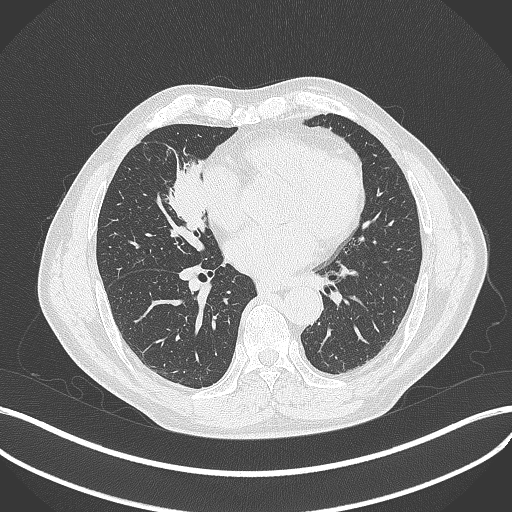
Chest CT, one axial slice; position 176 of 429 along the scan axis; reconstruction kernel B70f; 120 kVp; lung window (W 1500 / L -600 HU); 1 mm slice thickness; 512 × 512 image matrix. Patient: male, 61 years. Case-level facts recorded for this patient, not image findings: clinical TNM (as recorded): T2b N1 M0.
Annotated regions visible in this slice (rectangle marked by the reading radiologist):
- lung tumour (recorded histology: squamous cell carcinoma): bounding box <167,157,211,236> (left, top, right, bottom; pixels)